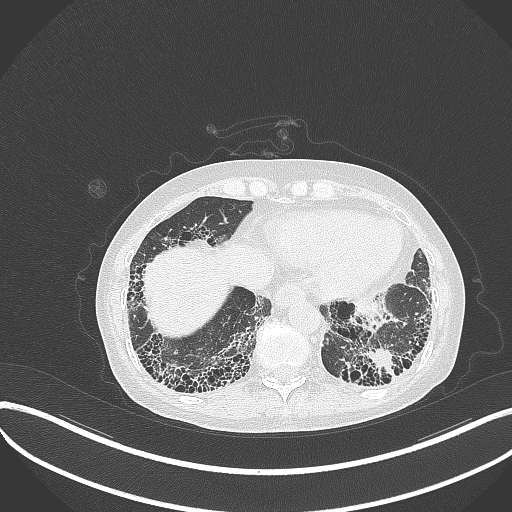
Chest CT, one axial slice; position 67 of 373 along the scan axis; reconstruction kernel B70f; 120 kVp; lung window (W 1500 / L -600 HU); 512 × 512 image matrix, field of view 400 × 400 mm. Female patient, age 56 years. Case-level facts recorded for this patient, not image findings: clinical TNM (as recorded): T1 N0 M0.
Annotated regions visible in this slice (bounding box drawn by a radiologist):
- lung tumour (recorded histology: adenocarcinoma): bounding box <366,345,401,380> (left, top, right, bottom; pixels)